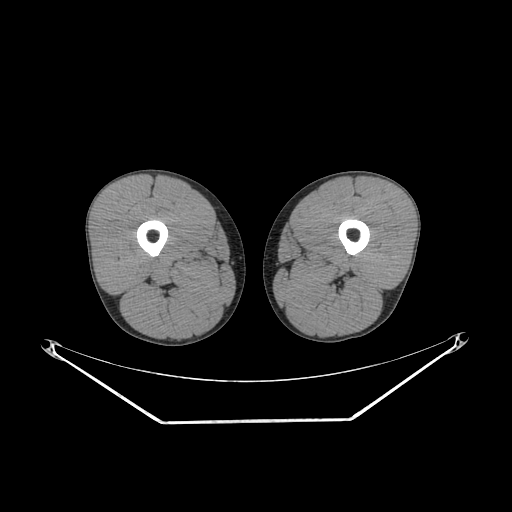
CT of an extremity soft-tissue mass (from a PET/CT study), one axial slice; position 217 of 267 along the scan axis; 140 kVp; soft-tissue window (W 400 / L 40 HU); 3.75 mm slice thickness; 512 × 512 image matrix, field of view 500 × 500 mm. Male patient. Case-level facts recorded for this patient, not image findings: histological type: extraskeletal osteosarcoma; grade: high; site of the primary tumour: left adductur.
Structures marked on this image (expert contour drawn on MRI and transferred to this co-registered scan by the dataset authors):
- gross tumour volume (mass): bounding box <285,251,353,280> (left, top, right, bottom; pixels)